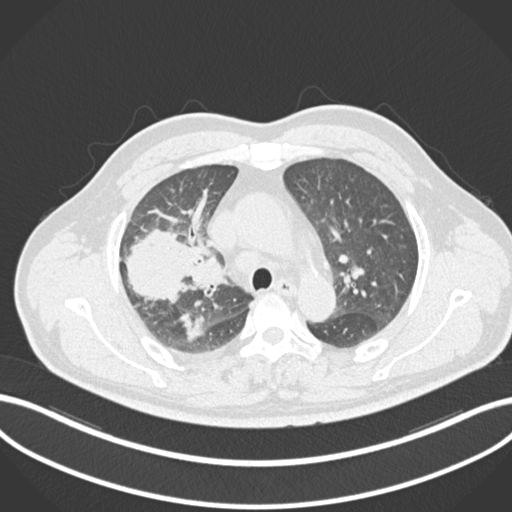
Chest CT, one axial slice; position 661 of 852 along the scan axis; 120 kVp; lung window (W 1500 / L -600 HU); 512 × 512 image matrix, field of view 400 × 400 mm. Male patient, age 55 years. Case-level facts recorded for this patient, not image findings: clinical TNM (as recorded): T3 N2 M1.
Outlined on this slice (bounding box drawn by a radiologist):
- lung tumour (recorded histology: adenocarcinoma): box from (x=120, y=223) to (x=199, y=306) px